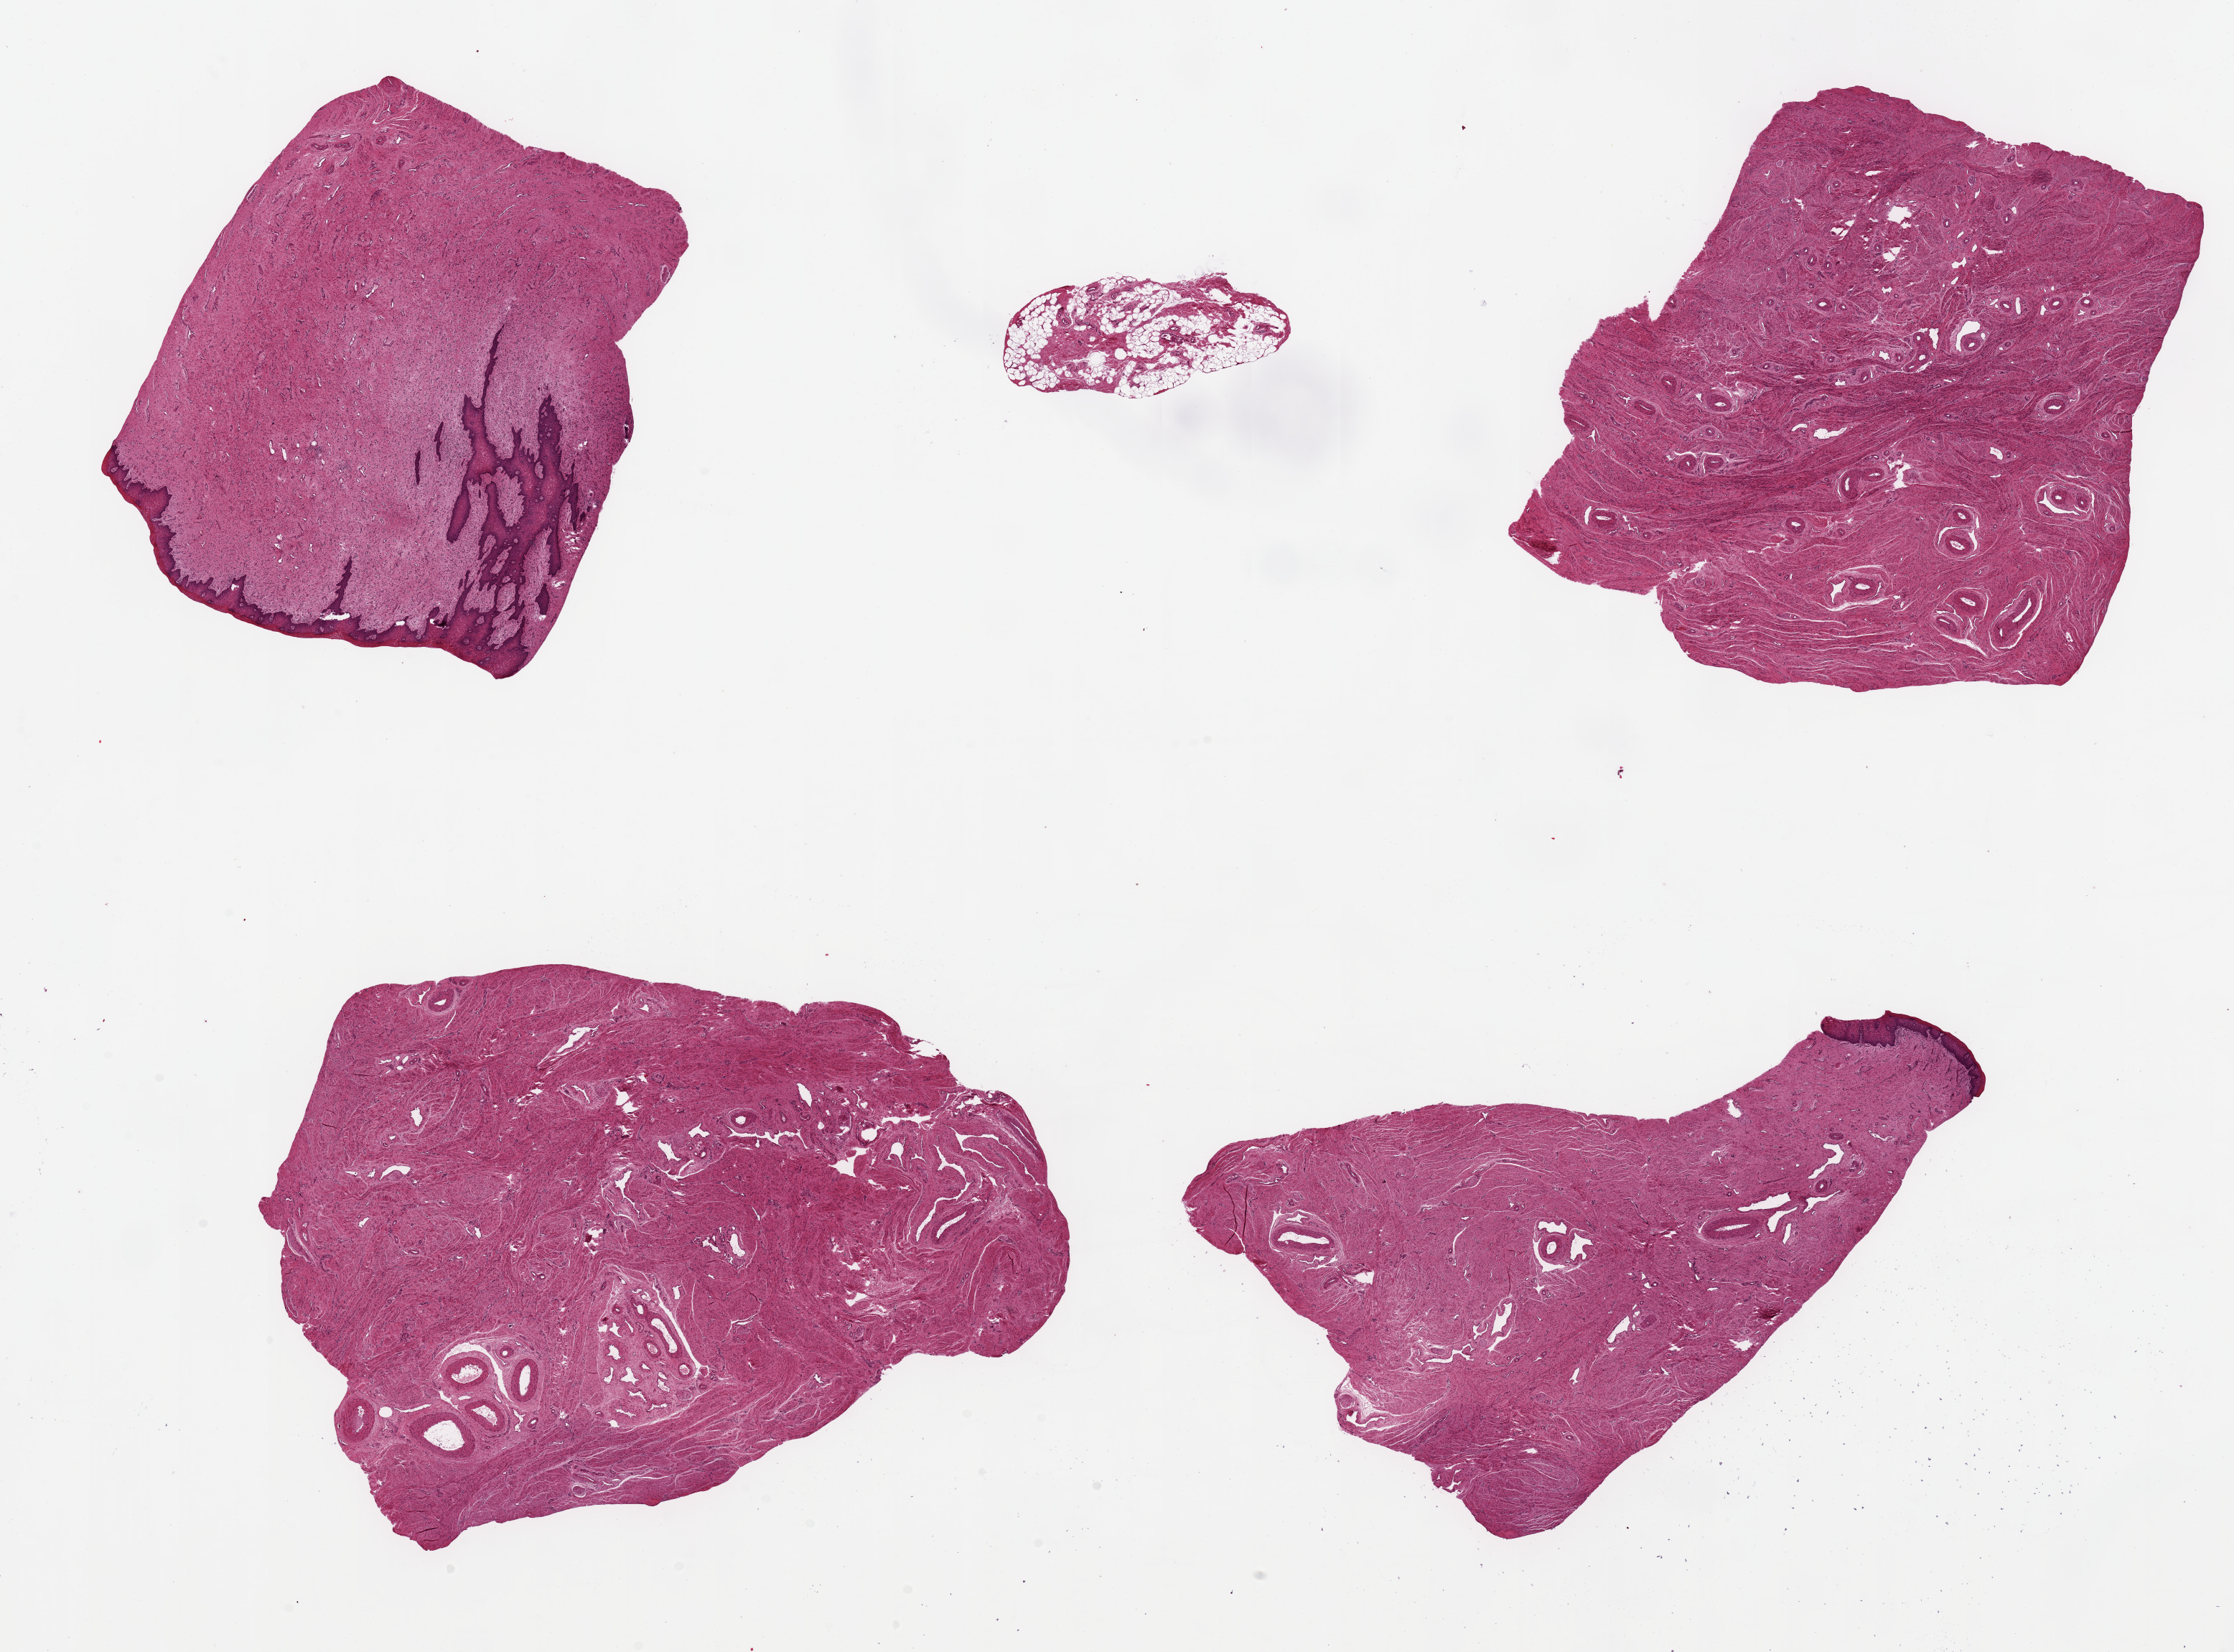
Whole-slide image, H&E stain, brightfield, low-resolution overview of the scanned area, about 24.6 x 18.2 mm; PAXgene-fixed paraffin-embedded (PFPE) section; sampled site (target tissue): exocervix; tissue donor sample. Female donor.
* review note (as recorded): 5 pieces, ~6x5mm, 2 ectocervix, 2 without epithelial lining; 1 3x1mm fibroadipose piece